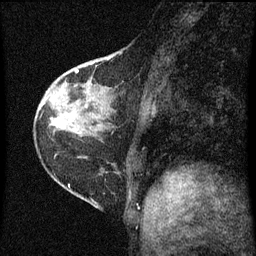
Breast MRI (dynamic contrast-enhanced), one sagittal slice. Position 23 of 60 along the scan axis. Dynamic contrast-enhanced series, image 2 of 3 at this slice position (ordered by acquisition). 1.5 T. TE 4.2 ms, TR 8 ms. 2 mm slice thickness. 256 × 256 image matrix, field of view 180 × 180 mm. Female patient, age 38 years.
Outlined on this slice (semi-automatic segmentation, software-assisted and operator-edited):
- analysis volume of interest (the breast-tissue region the enhancement analysis was run in; not a lesion): bounding box [x1, y1, x2, y2] px = [67, 48, 143, 131]
- tumour enhancement mask (voxels above the 70 % enhancement threshold inside the analysis volume of interest): [75, 70, 79, 73]